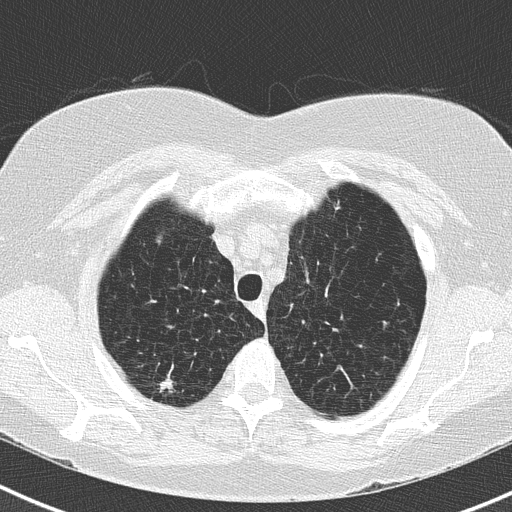
Chest CT (low-dose screening protocol), one axial image; second screening round (one year after baseline); lung window (W 1500 / L -600 HU); 120 kVp; slice 38 of 183 in the series. Female, age 73 years at enrolment. Former smoker at enrolment.
Lesion marked by an expert reader, bounding box <141,363,190,402> (left, top, right, bottom; pixels). The screening reader recorded 2 non-calcified nodules or masses ≥4 mm on this exam; which of them this box marks is not recorded. Official screen result: positive, no significant change: stable abnormalities potentially related to lung cancer, unchanged since the prior screening exam. Later outcome: lung cancer diagnosed 250 days after this screen — adenocarcinoma, NOS, right upper lobe, moderately differentiated (G2), stage IB (AJCC 6th edition), 15 mm at pathology.